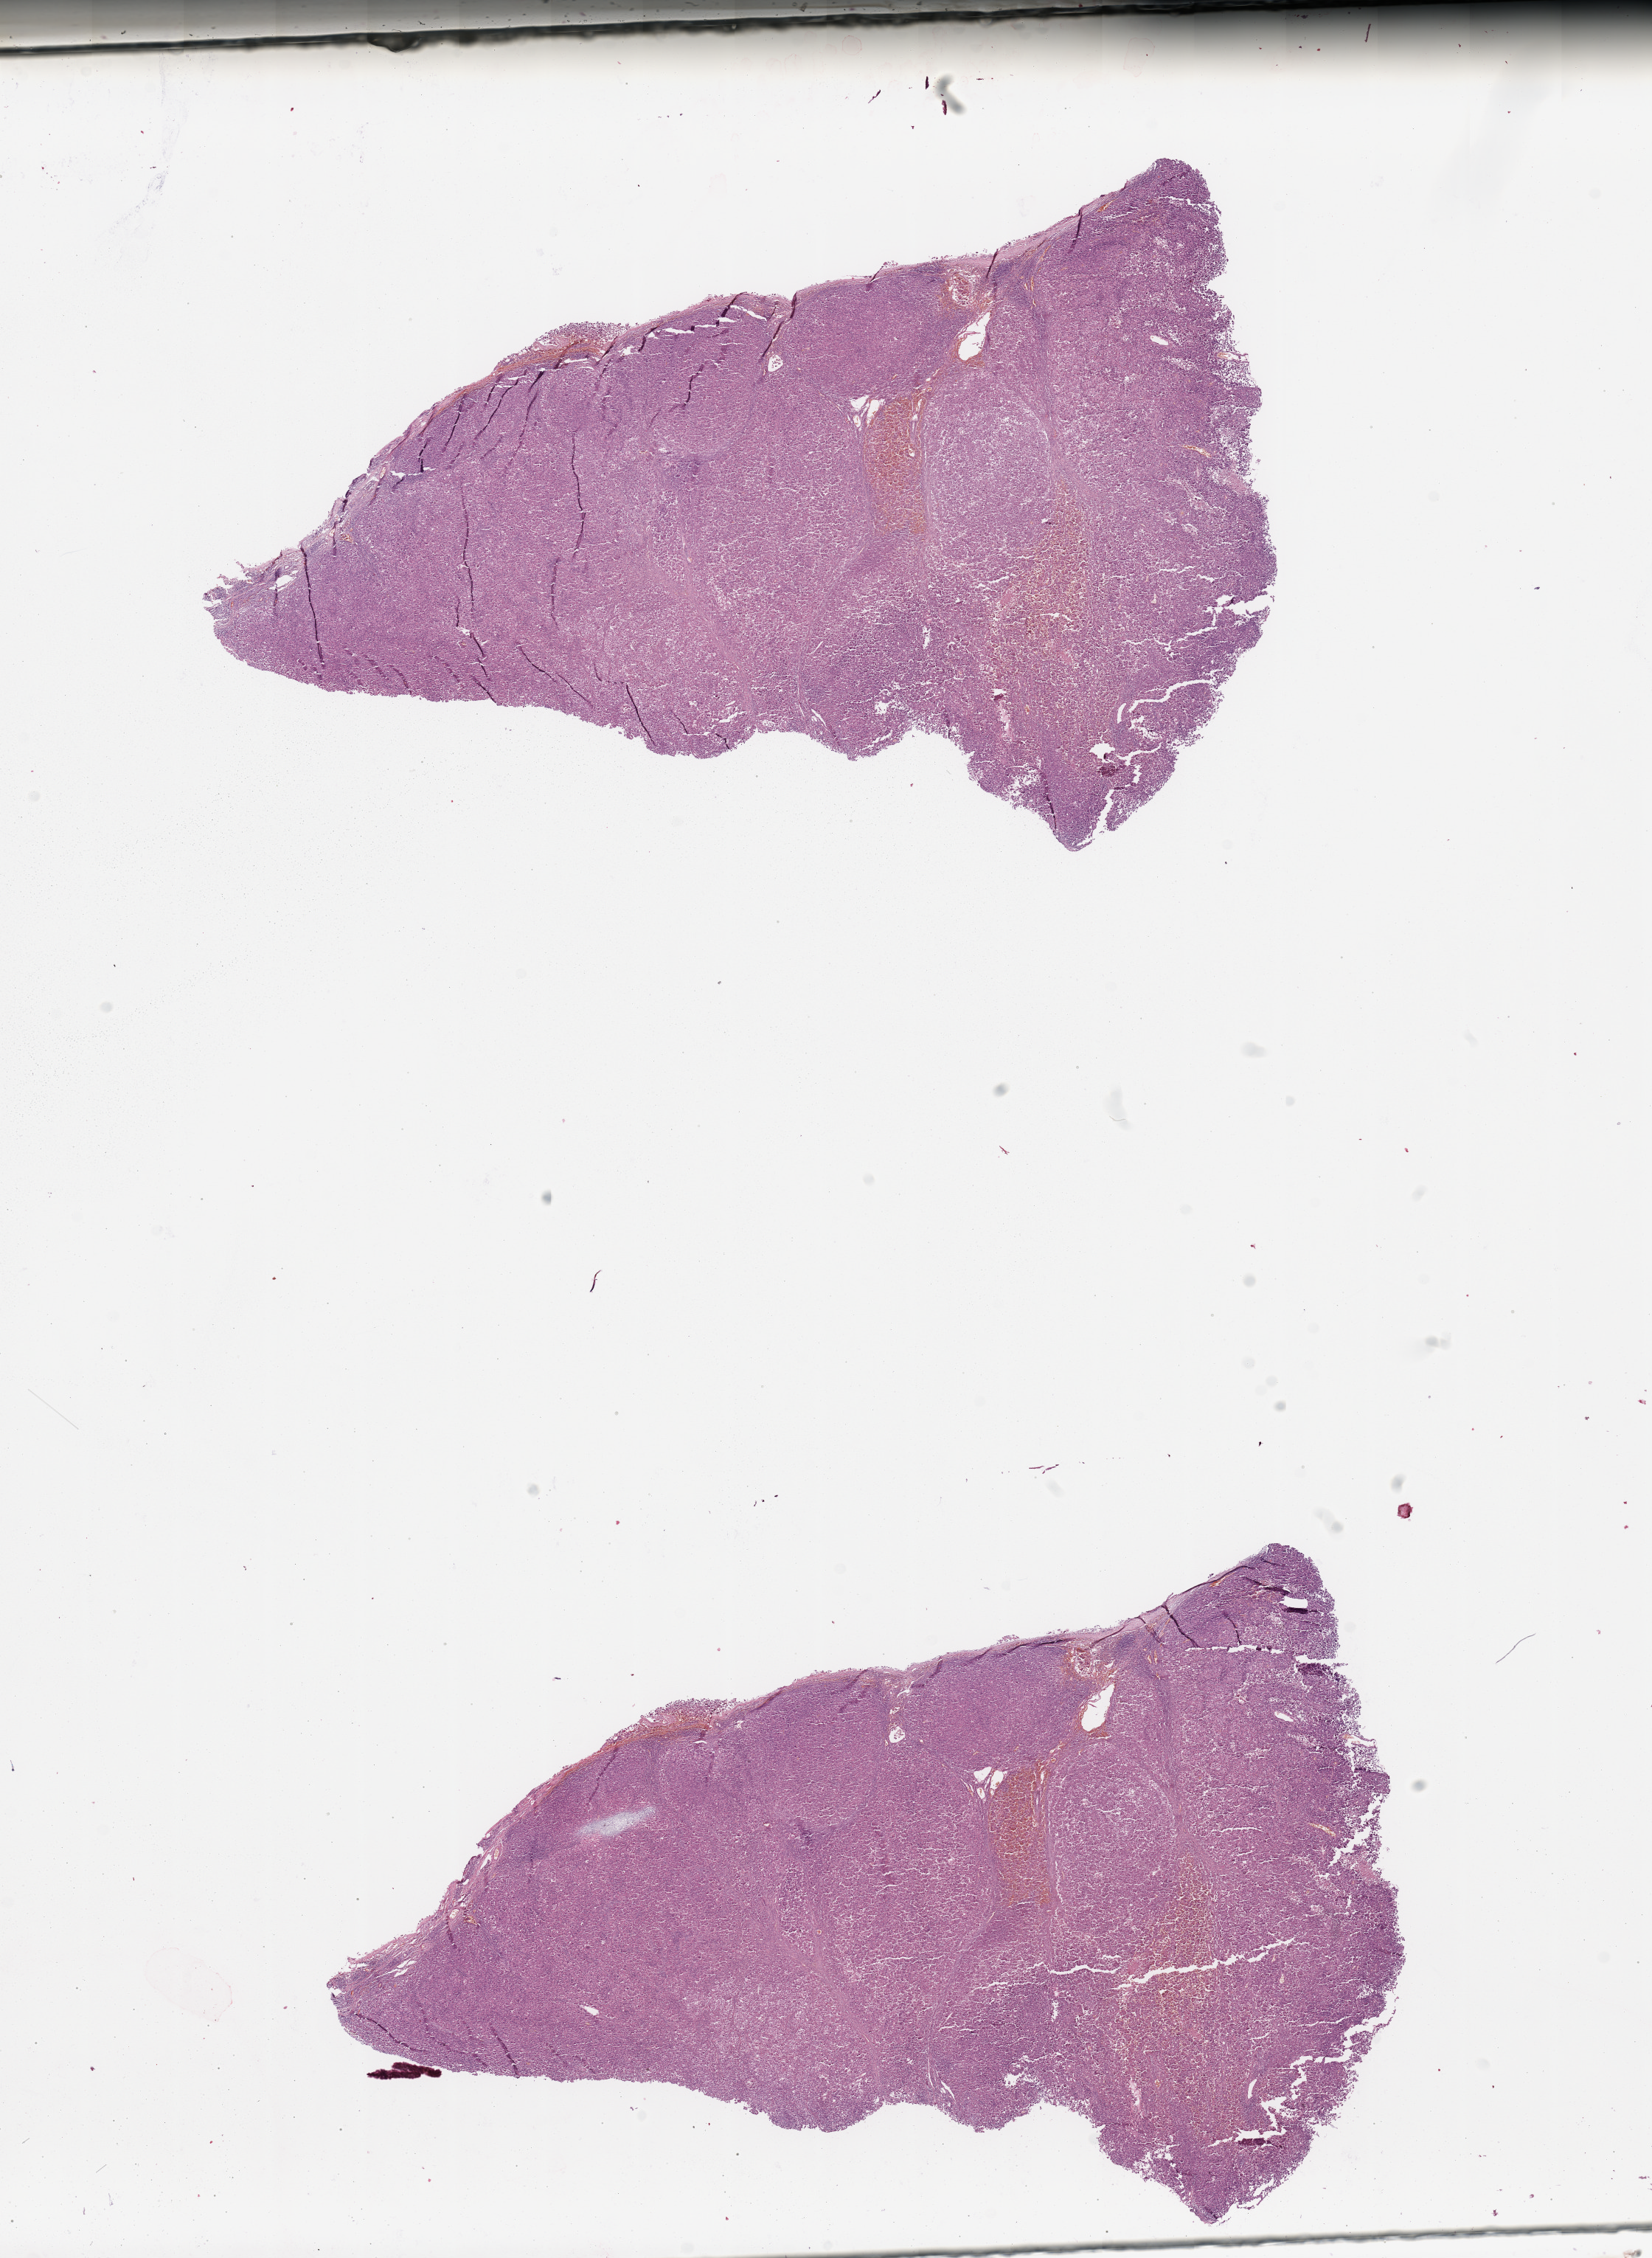
H&E-stained whole-slide image — whole scanned area (about 17.7 x 24.2 mm) shown as a low-resolution overview. Melanoma tumour tissue; sampled site not recorded. Patient: male, age 32 years.
- AJCC pathologic stage: IIB
- diagnosis: Malignant melanoma, NOS
- primary tumour site (as recorded): extremities